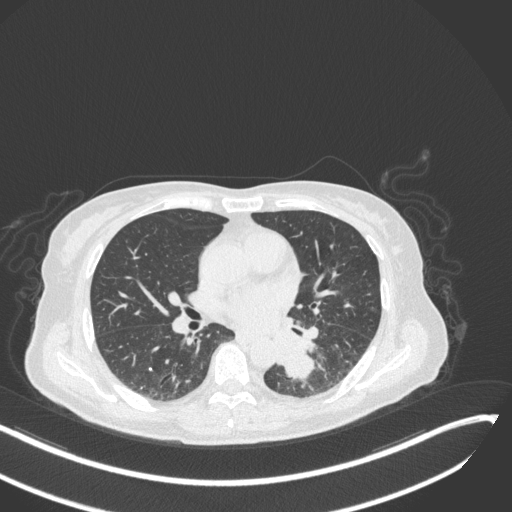
Chest CT, one axial slice; reconstruction kernel B31f; 120 kVp; lung window (W 1500 / L -600 HU); 1 mm slice thickness; 512 × 512 image matrix. Female patient, age 64 years. From the clinical record (not read from this slice): clinical TNM (as recorded): T3 N1 M1; histopathological grade: G3.
Annotated regions visible in this slice (rectangle marked by the reading radiologist):
- lung tumour (recorded histology: small cell carcinoma): bounding box [x1, y1, x2, y2] px = [275, 339, 323, 392]